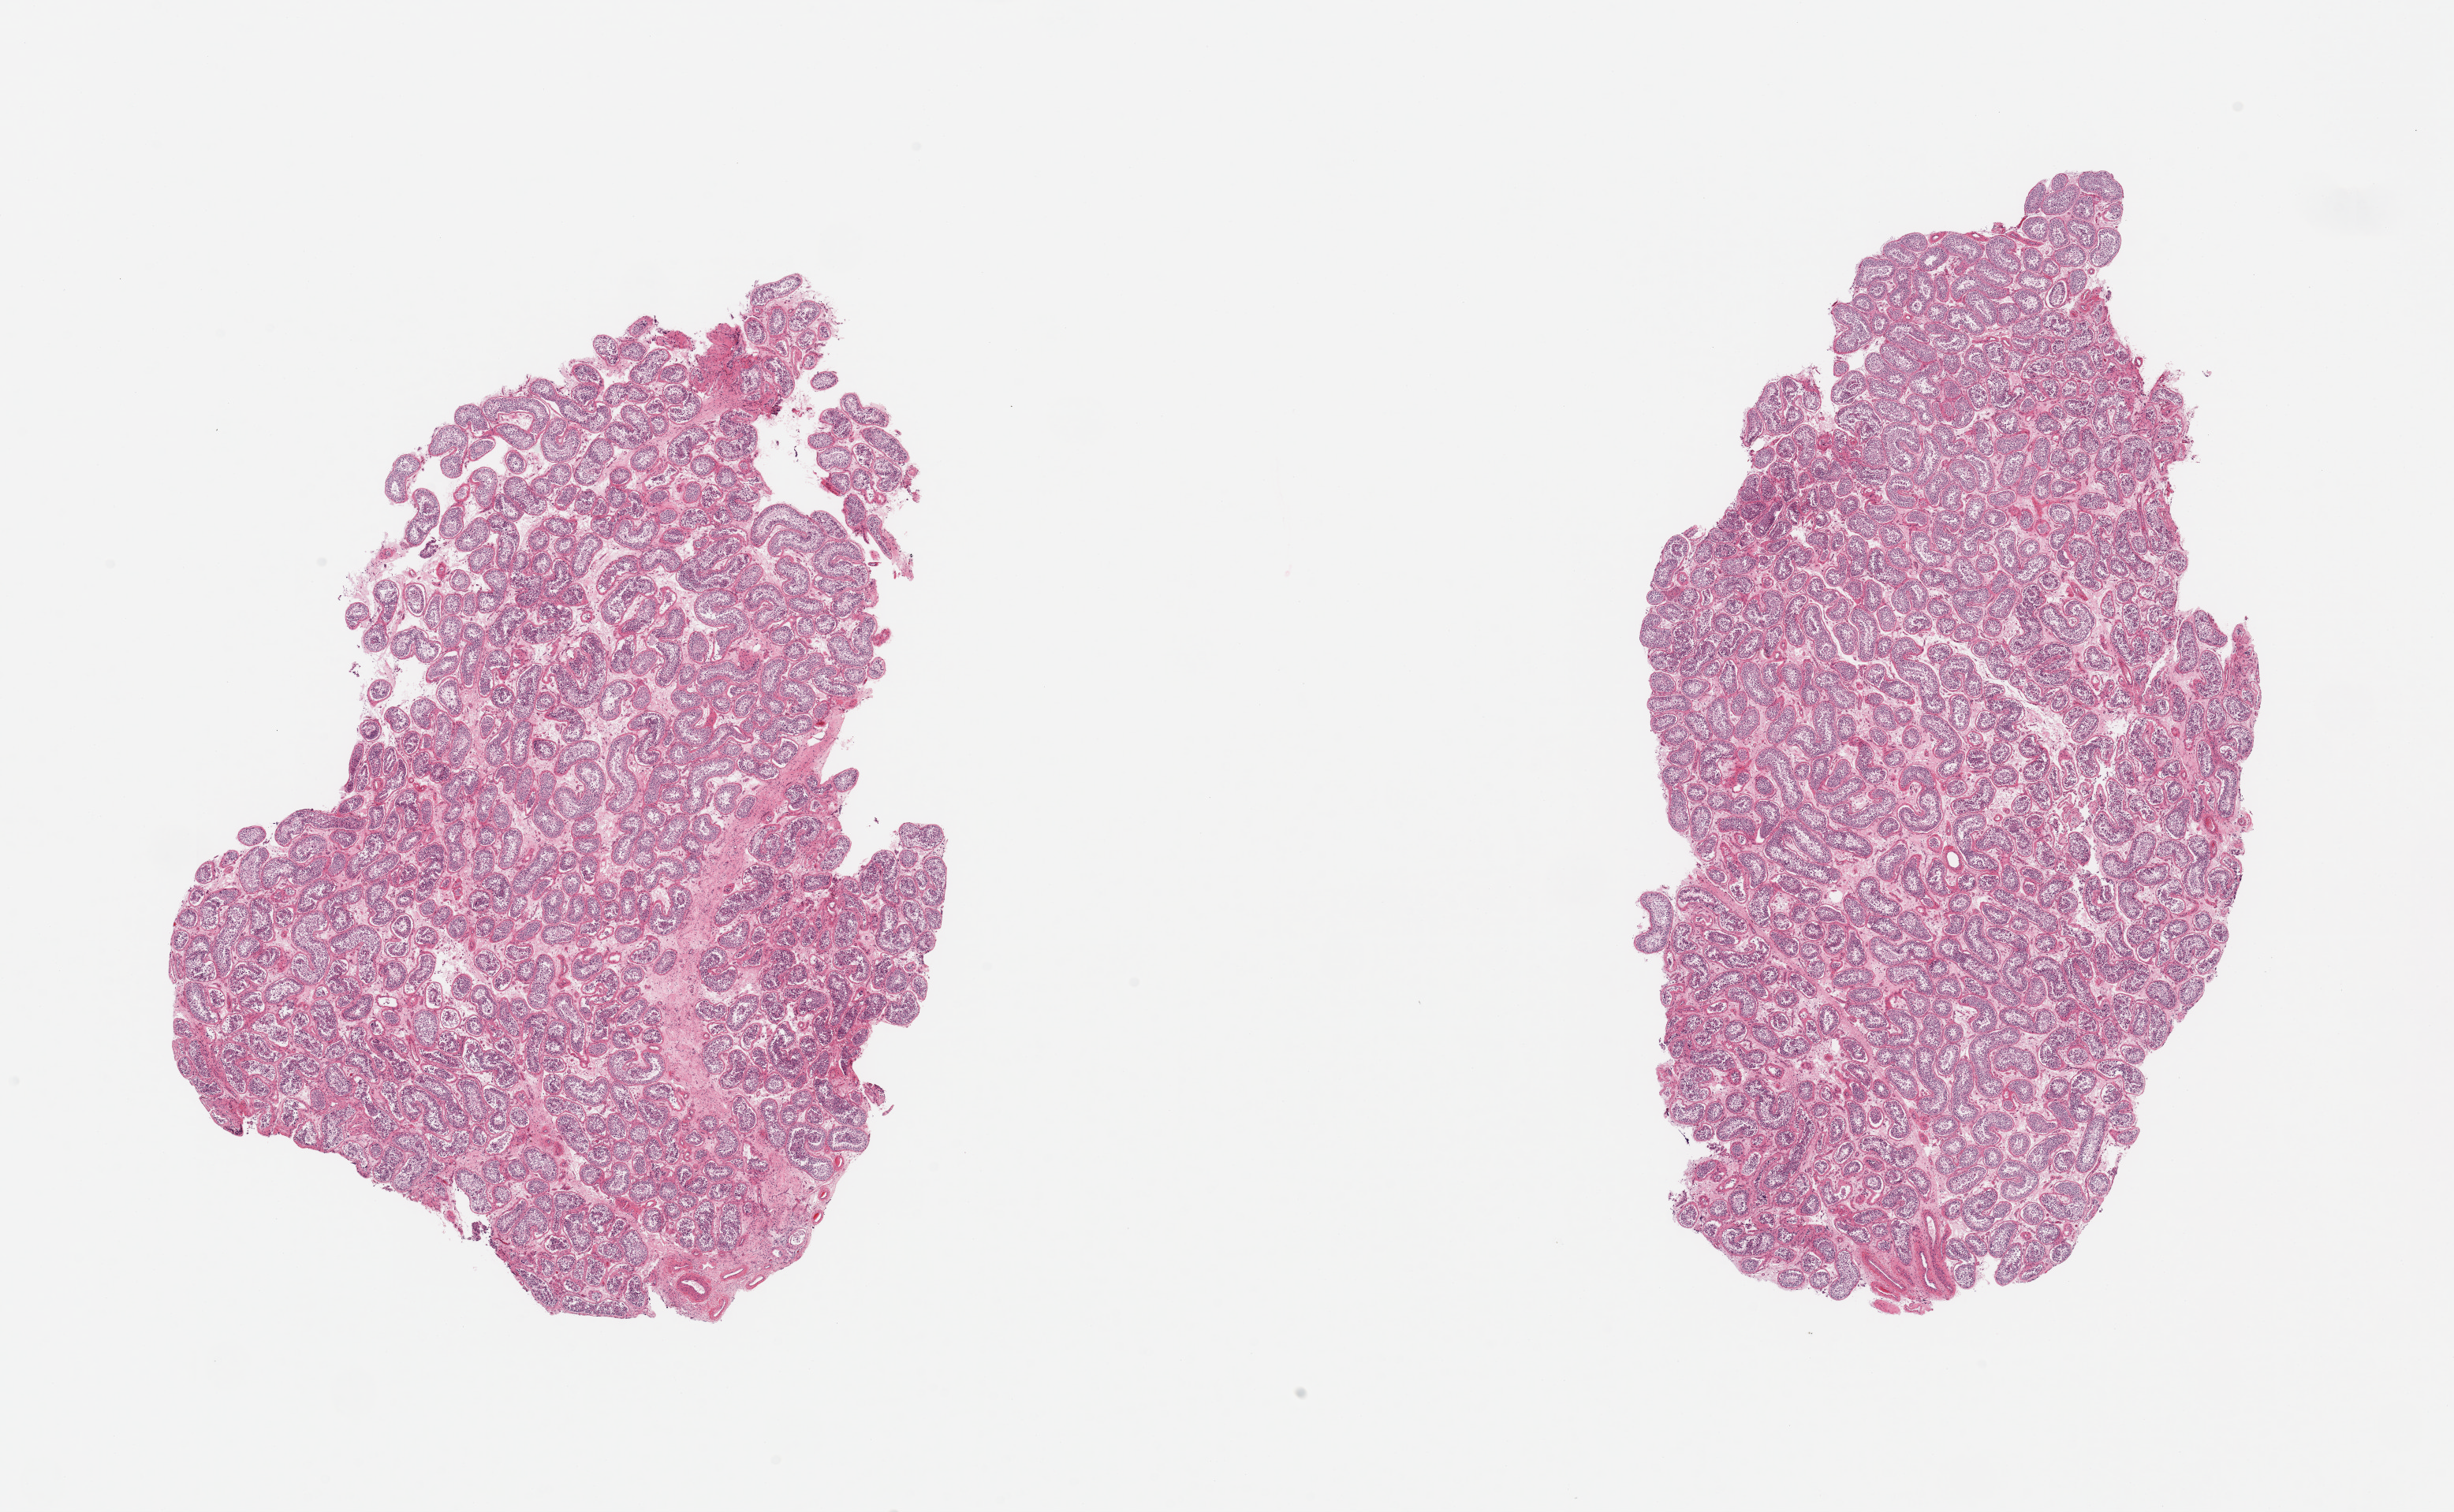
Haematoxylin and eosin whole-slide image, shown as a low-resolution overview of the whole scanned area (about 24.6 x 15.2 mm, slide scanned at 20x), PAXgene-fixed paraffin-embedded (PFPE) section, section of testis (target tissue), tissue donor sample. Male donor.
• review note (as recorded): 2 pieces; active spermatogenesis